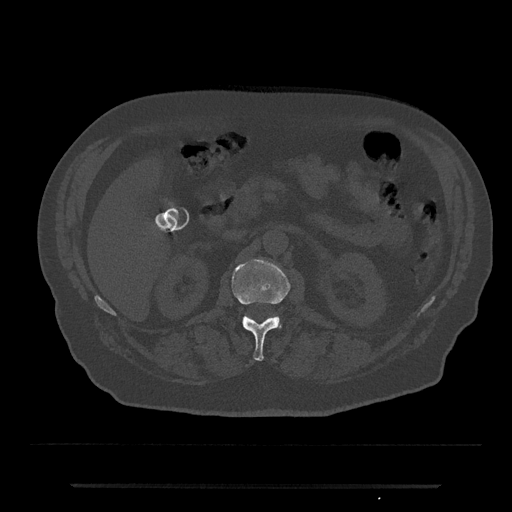
CT including the spine, one axial slice; position 523 of 797 along the scan axis; 120 kVp; bone window (W 1800 / L 400 HU); 512 × 512 image matrix. Patient: male, 80 years. From the clinical record (not read from this slice): primary cancer: prostate.
Outlined on this slice (semi-automatic segmentation, software-assisted and operator-edited):
- L1 vertebra: bounding box (x1, y1, x2, y2) in pixels: (232, 259, 291, 361)